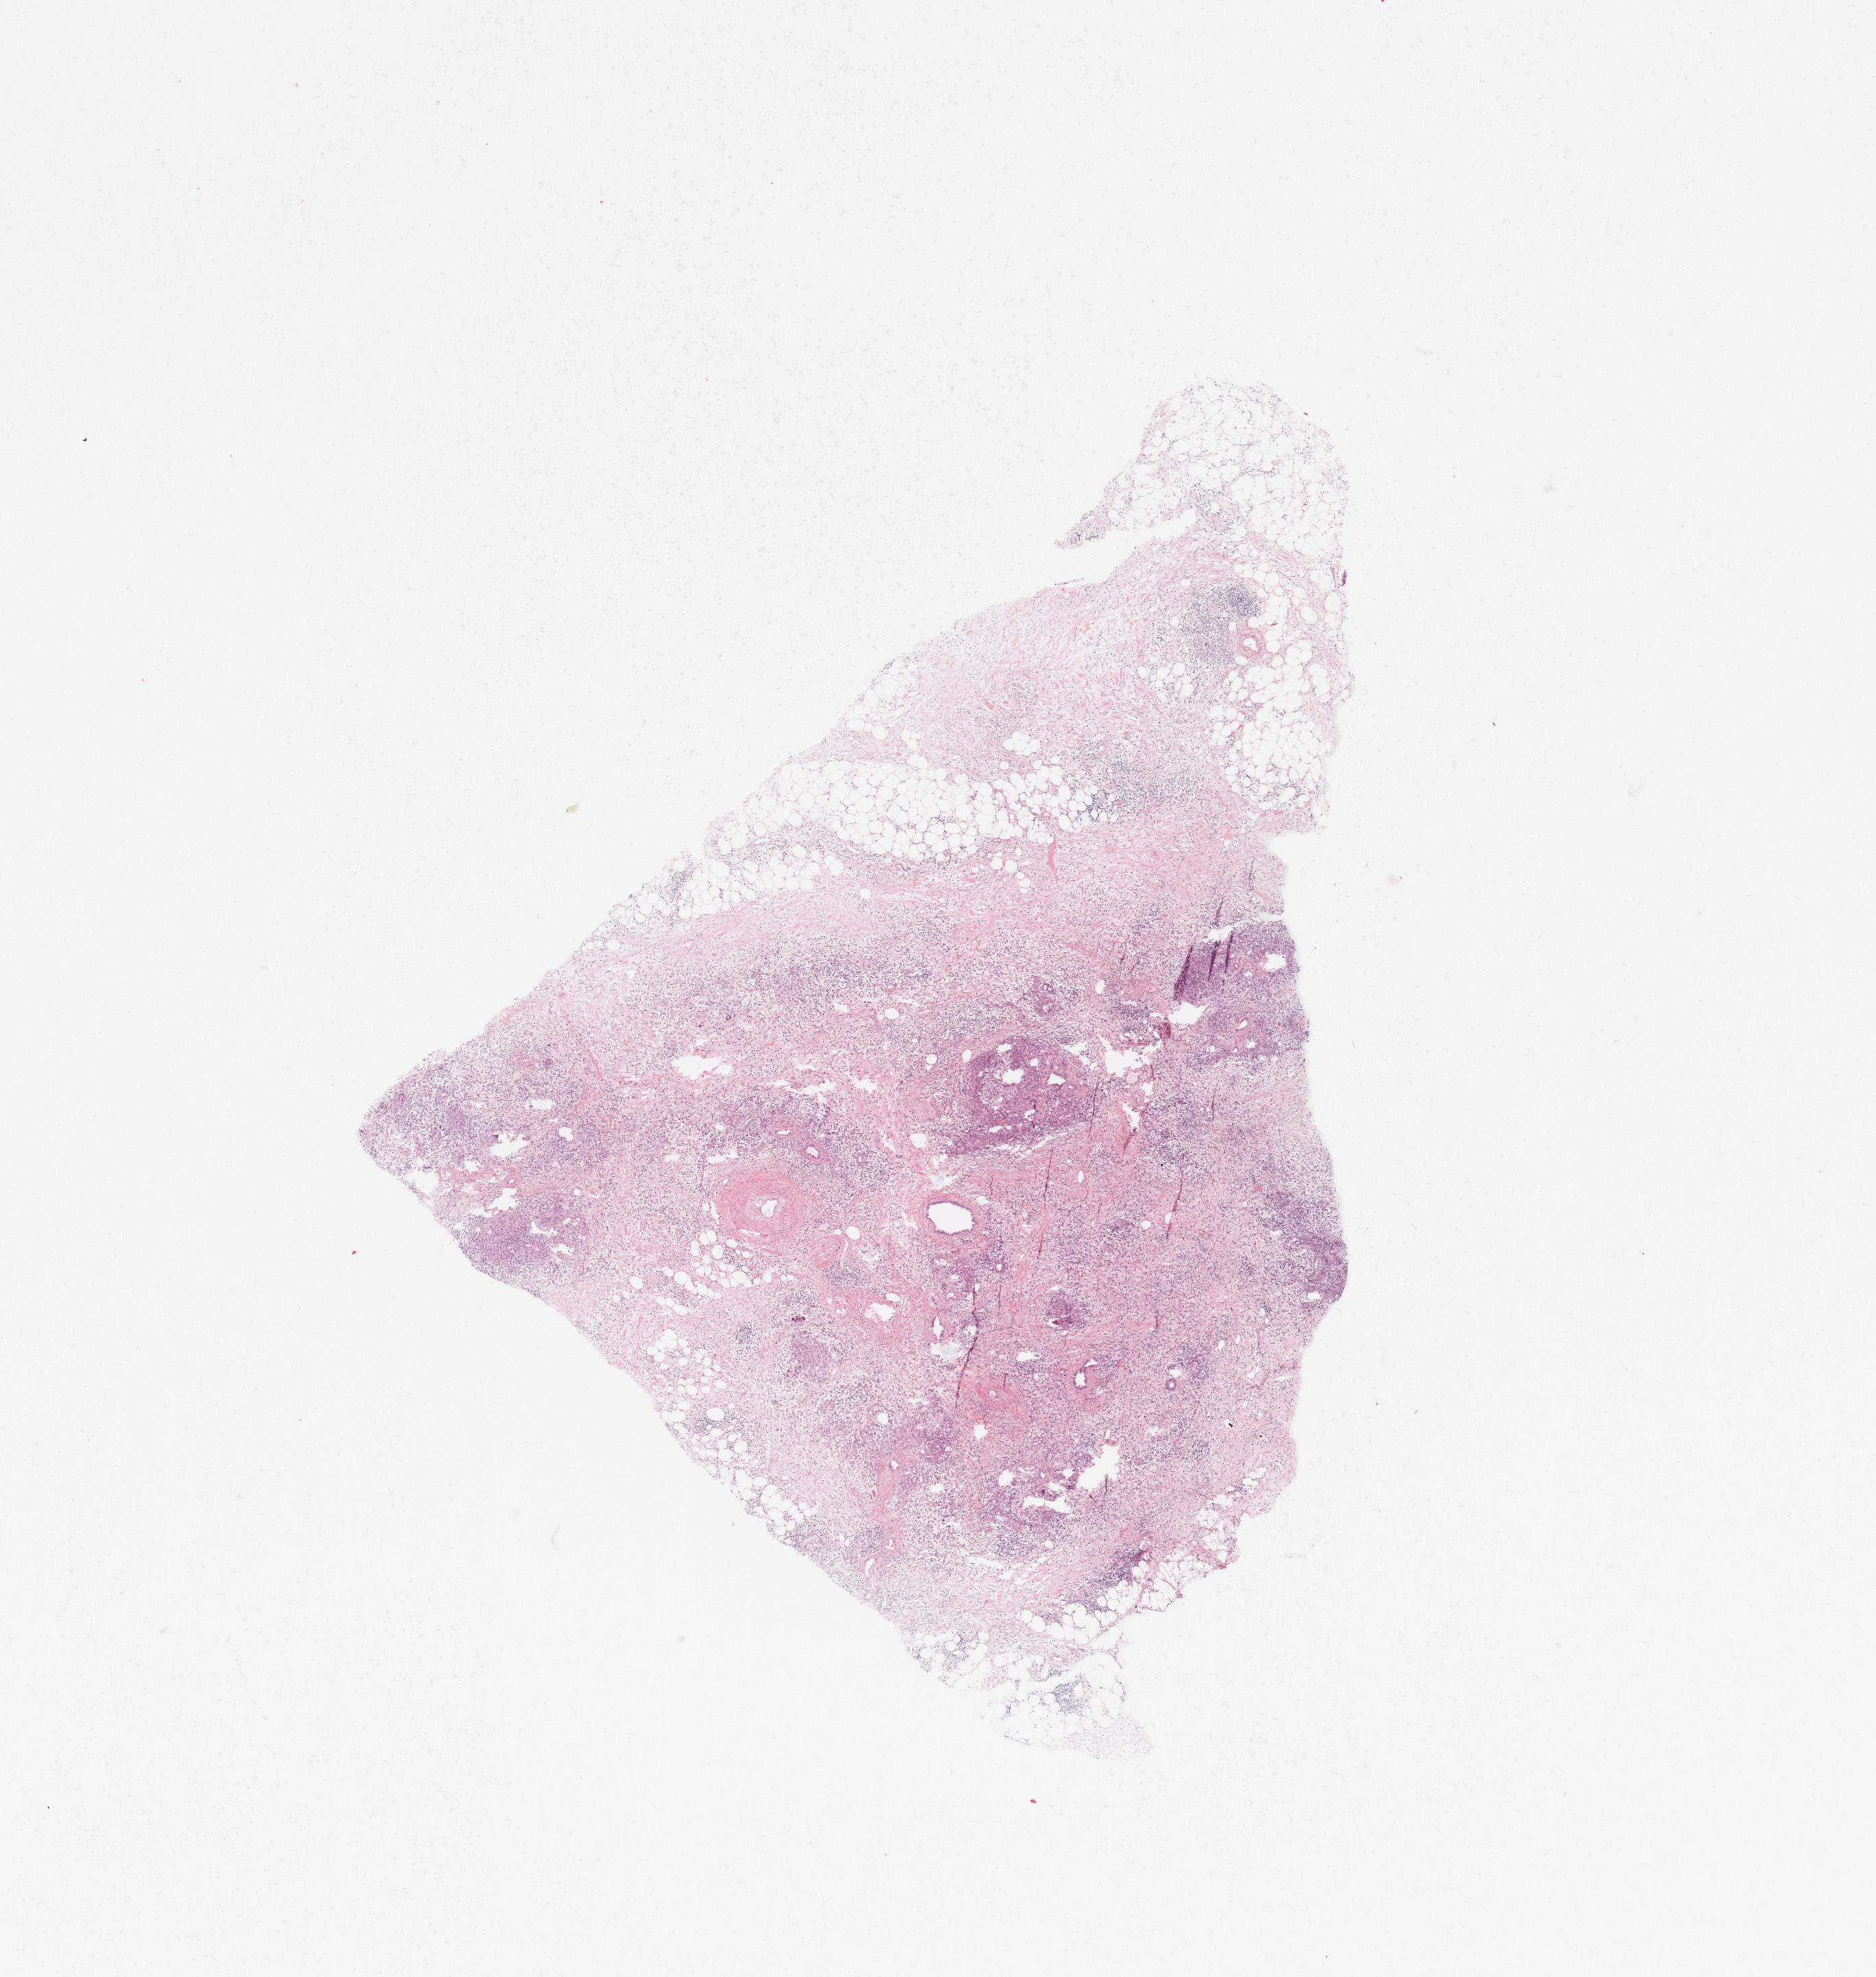
H&E whole-slide image, low-resolution overview of the scanned area, about 10.8 x 11.4 mm (slide scanned at 20x); pancreas, tumour tissue. 51-year-old female patient. Histologic grade: G2 (moderately differentiated).
Primary tumour site (as recorded): head. Histologic diagnosis: Infiltrating duct carcinoma, NOS. AJCC pathologic stage: IA.